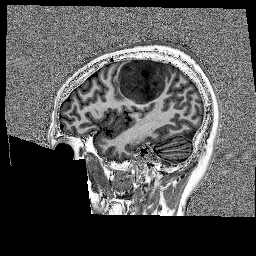
Brain MRI from a brain-tumour surgery series, one sagittal slice; position 48 of 176 along the scan axis; 1 mm slice thickness; 256 × 256 image matrix, field of view 256 × 256 mm. Case-level facts recorded for this patient, not image findings: histopathology: Glioblastoma; WHO grade: 4; IDH mutation: no; tumour location: Left Frontal.
Annotated regions visible in this slice (outlined manually by an expert reader):
- tumour: box from (x=118, y=58) to (x=175, y=105) px